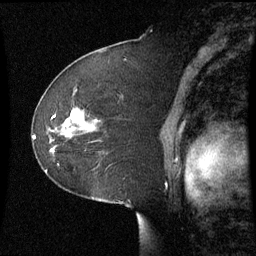
Breast MRI (dynamic contrast-enhanced), one sagittal slice. Position 41 of 60 along the scan axis. Dynamic contrast-enhanced series, image 2 of 3 at this slice position (ordered by acquisition). 1.5 T. TE 4.2 ms, TR 8.9 ms. 2.2 mm slice thickness. 256 × 256 image matrix, field of view 220 × 220 mm. Patient: female, 51 years. Case-level facts recorded for this patient, not image findings: setting: breast cancer imaged before/during neoadjuvant chemotherapy; receptor status: HR-positive, HER2-negative.
Structures marked on this image (semi-automatically segmented with operator editing):
- analysis volume of interest (the breast-tissue region the enhancement analysis was run in; not a lesion): bounding box [x1, y1, x2, y2] px = [50, 108, 97, 165]
- tumour enhancement mask (voxels above the 70 % enhancement threshold inside the analysis volume of interest): [66, 110, 85, 127]